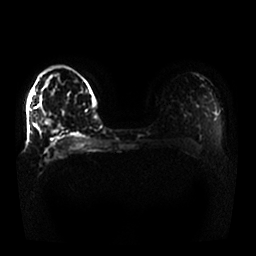
Breast MRI, one axial slice; position 11 of 25 along the scan axis; diffusion-weighted series; image 2 of 4 stored at this slice position (different b-values; order by instance number); 1.5 T; 4 mm slice thickness; 256 × 256 image matrix, field of view 370 × 370 mm. Female patient.
Annotated regions visible in this slice (expert manual segmentation):
- tumour on diffusion-weighted imaging: bounding box [x1, y1, x2, y2] px = [45, 120, 51, 126]